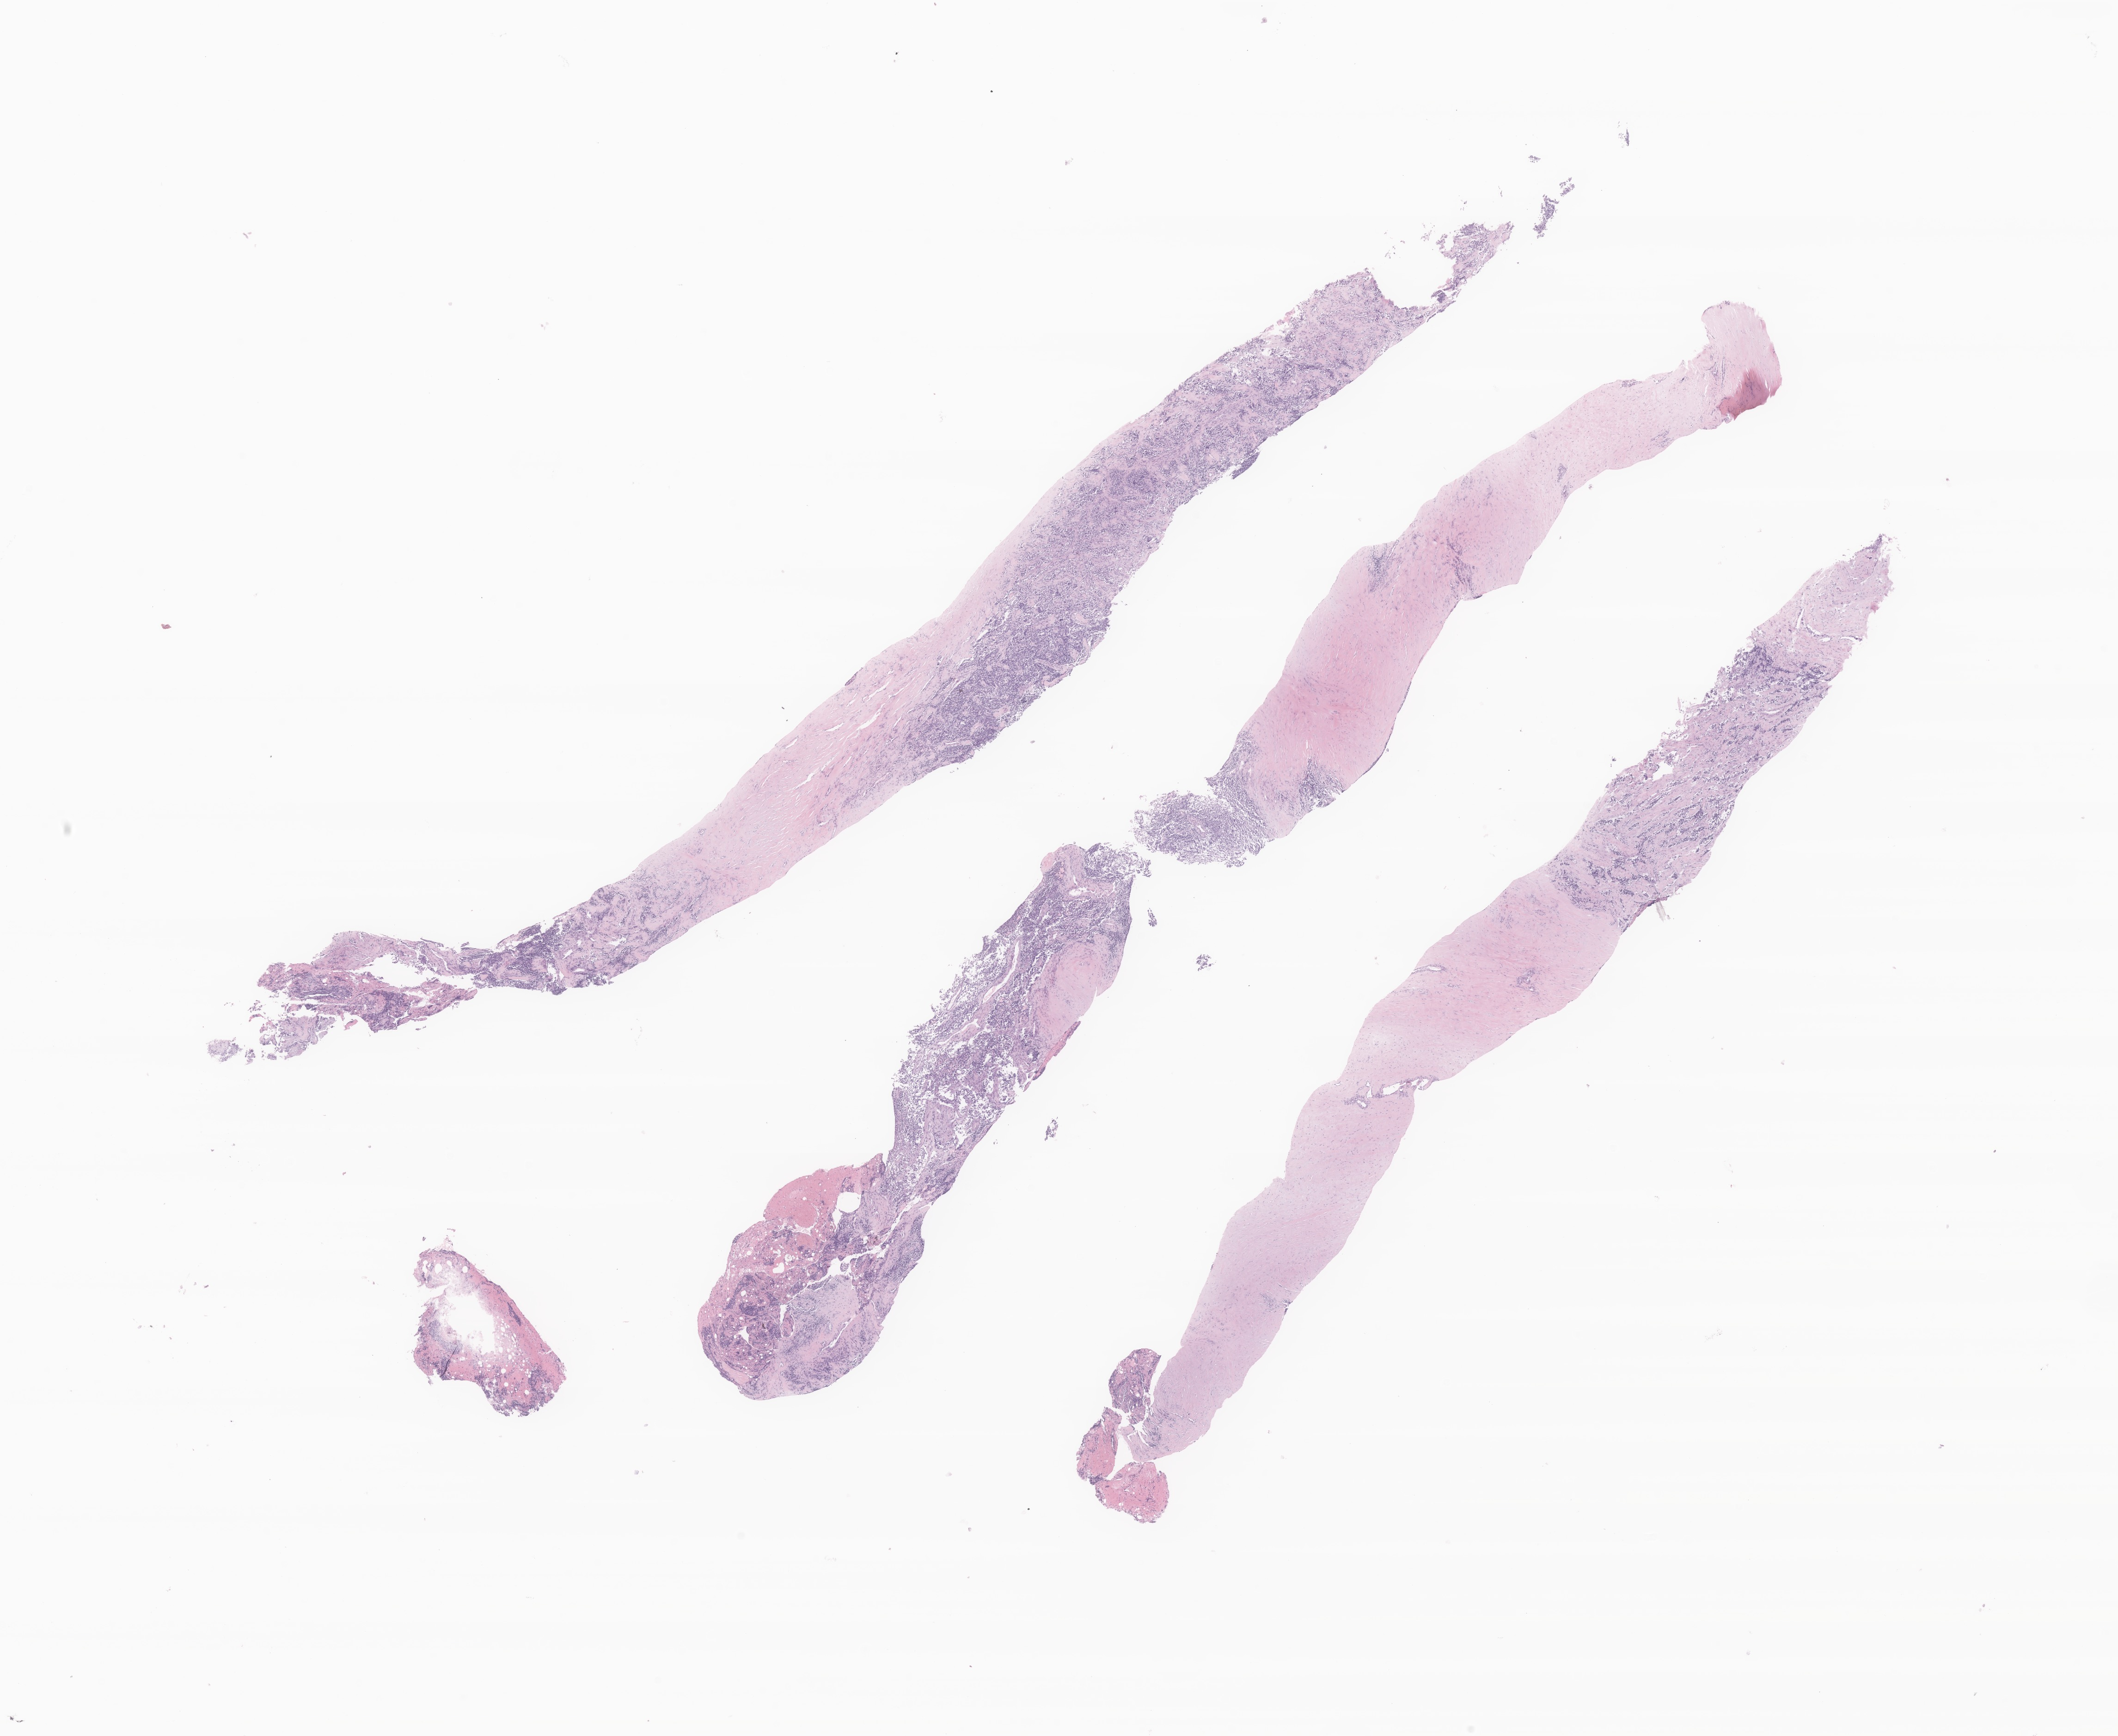
Digitized H&E-stained section of tumor tissue from the soft tissue — a low-resolution overview of the entire scanned area, about 19.3 x 15.8 mm, formalin-fixed, paraffin-embedded (FFPE) tissue. Male patient, age 134 months.
Diagnosis (ICD-O-3 morphology term): Alveolar rhabdomyosarcoma.